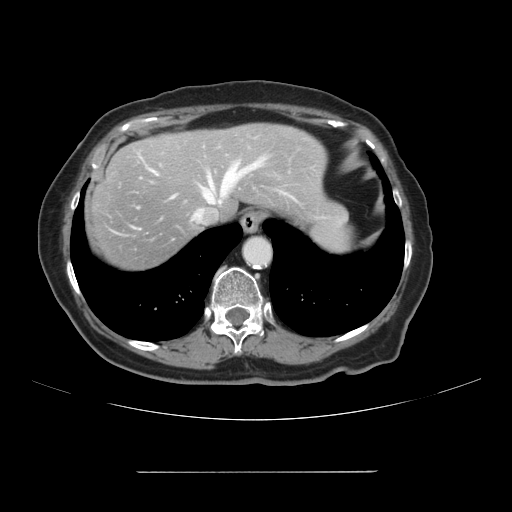
Contrast-enhanced abdominal CT, one axial slice; slice 91 of 111 in the series (ordered by position); 120 kVp; soft-tissue window (W 400 / L 40 HU); 2.5 mm slice thickness; 512 × 512 image matrix, field of view 400 × 400 mm. Female patient, age 74 years. Case-level facts recorded for this patient, not image findings: diagnosis: colorectal cancer liver metastases, imaged before liver resection.
Structures marked on this image (outlined manually by an expert reader):
- hepatic veins: bounding box [x1, y1, x2, y2] px = [152, 159, 264, 221]
- liver: [89, 123, 338, 272]
- planned liver remnant (the part of the liver to remain after resection): [174, 123, 339, 217]
- portal vein (with intrahepatic branches): [205, 184, 222, 201]